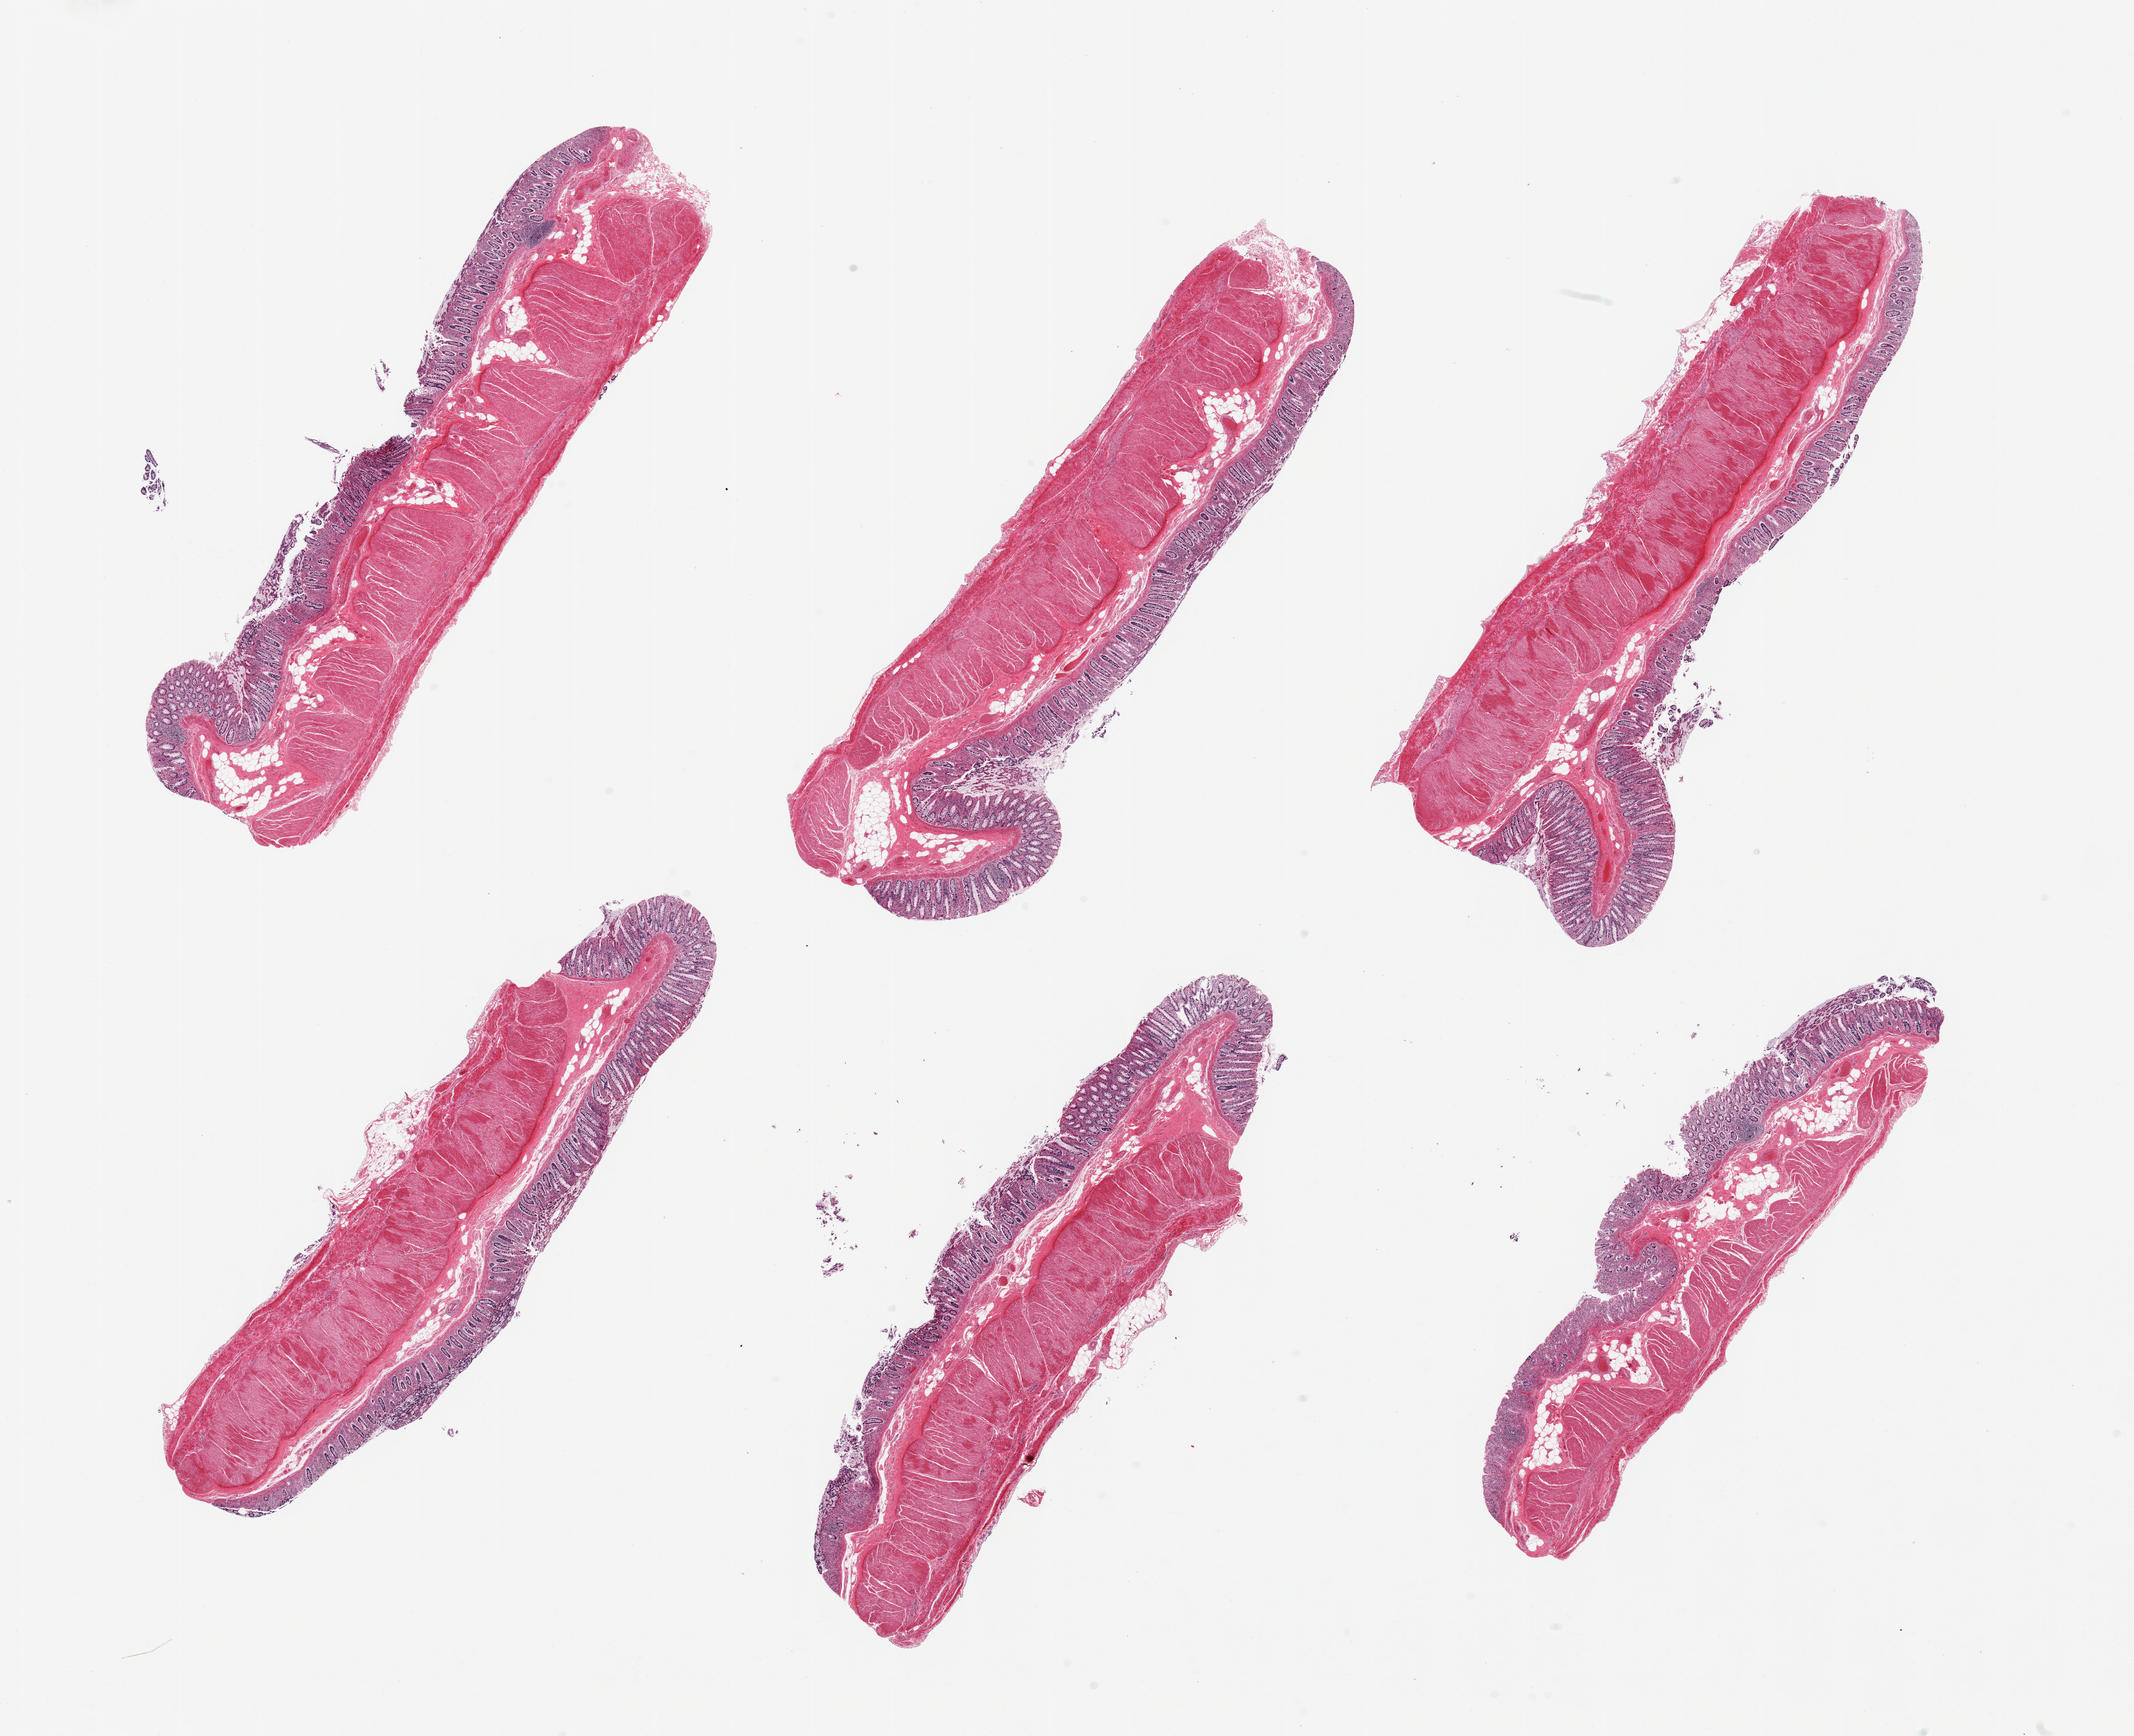
Hematoxylin and eosin (H&E) whole-slide image, low-resolution overview of the scanned area, about 26.6 x 21.6 mm (slide scanned at 20x). PAXgene-fixed, paraffin-embedded tissue. Section of transverse colon (target tissue). Donor tissue sample. Donor: male.
* pathologist's review note for this sample: 6 pieces, target mucosa is ~0.5mm, ~15-20% thickness